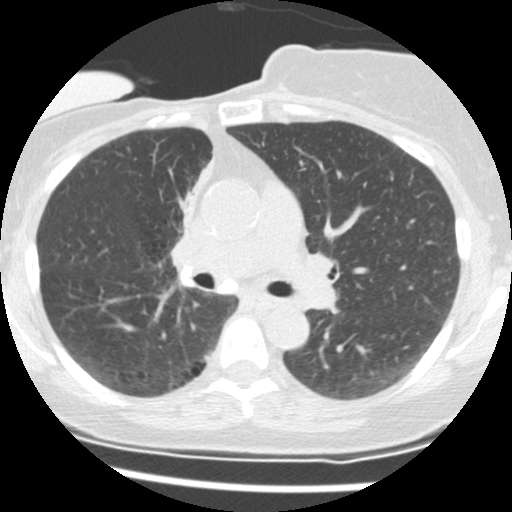
Axial slice from a low-dose chest CT screening exam. Second annual screen. Lung window (W 1500 / L -600 HU). 2.5 mm slice thickness. Female, age 56 years at enrolment. Current smoker at enrolment.
- Expert-annotated lung lesion, bounding box (x1, y1, x2, y2) in pixels: (151, 156, 205, 253).
- The screening reader recorded 2 non-calcified nodules or masses ≥4 mm on this exam; which of them this box marks is not recorded.
- Official screen result: positive, change unspecified: nodule(s) >= 4 mm or enlarging nodule(s), mass(es), or other non-specific abnormalities suspicious for lung cancer.
- Lung cancer was diagnosed 675 days after this screen (after the third annual screen): adenocarcinoma, NOS, right upper lobe, stage IIIB (AJCC 6th edition), 8 mm at pathology.